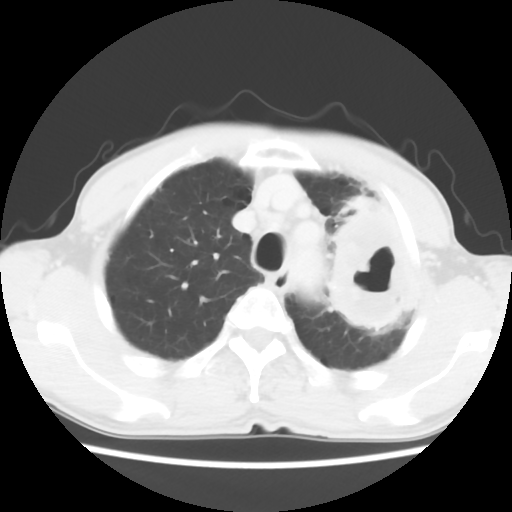
Chest CT, one axial slice; position 47 of 60 along the scan axis; lung window (W 1500 / L -600 HU); 5 mm slice thickness; 512 × 512 image matrix. Patient: male, 64 years. From the clinical record (not read from this slice): clinical TNM (as recorded): T3 N3 M0; histopathological grade: G3.
Structures marked on this image (rectangle marked by the reading radiologist):
- lung tumour (recorded histology: adenocarcinoma): bounding box <322,193,428,339> (left, top, right, bottom; pixels)